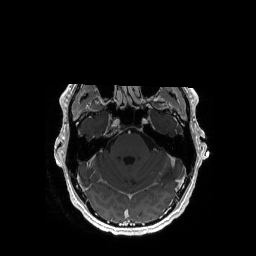
Brain MRI from a brain-tumour surgery series, one axial slice. Slice 124 of 192 in the series (ordered by position). T1-weighted post-contrast. 1 mm slice thickness. 256 × 256 image matrix, field of view 256 × 256 mm. Case-level facts recorded for this patient, not image findings: histopathology: Astrocytoma; WHO grade: 3; IDH mutation: yes.
Outlined on this slice (expert manual segmentation):
- tumour: bounding box <156,124,171,179> (left, top, right, bottom; pixels)